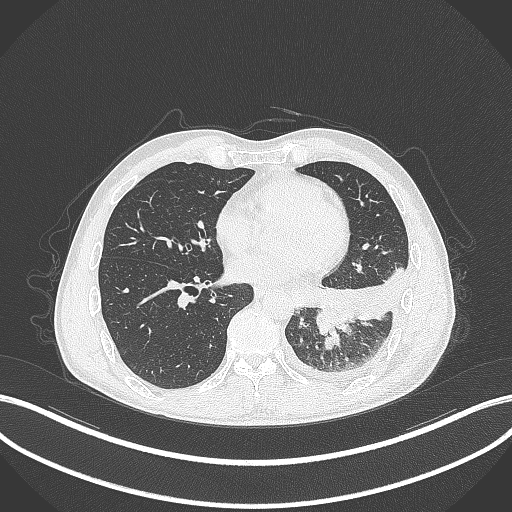
Chest CT, one axial slice; position 123 of 295 along the scan axis; lung window (W 1500 / L -600 HU); 1 mm slice thickness; 512 × 512 image matrix, field of view 400 × 400 mm. Patient: male, 47 years. From the clinical record (not read from this slice): clinical TNM (as recorded): T3 N1 M1c.
Annotated regions visible in this slice (rectangle marked by the reading radiologist):
- lung tumour (recorded histology: small cell carcinoma): bounding box [x1, y1, x2, y2] px = [315, 302, 357, 336]